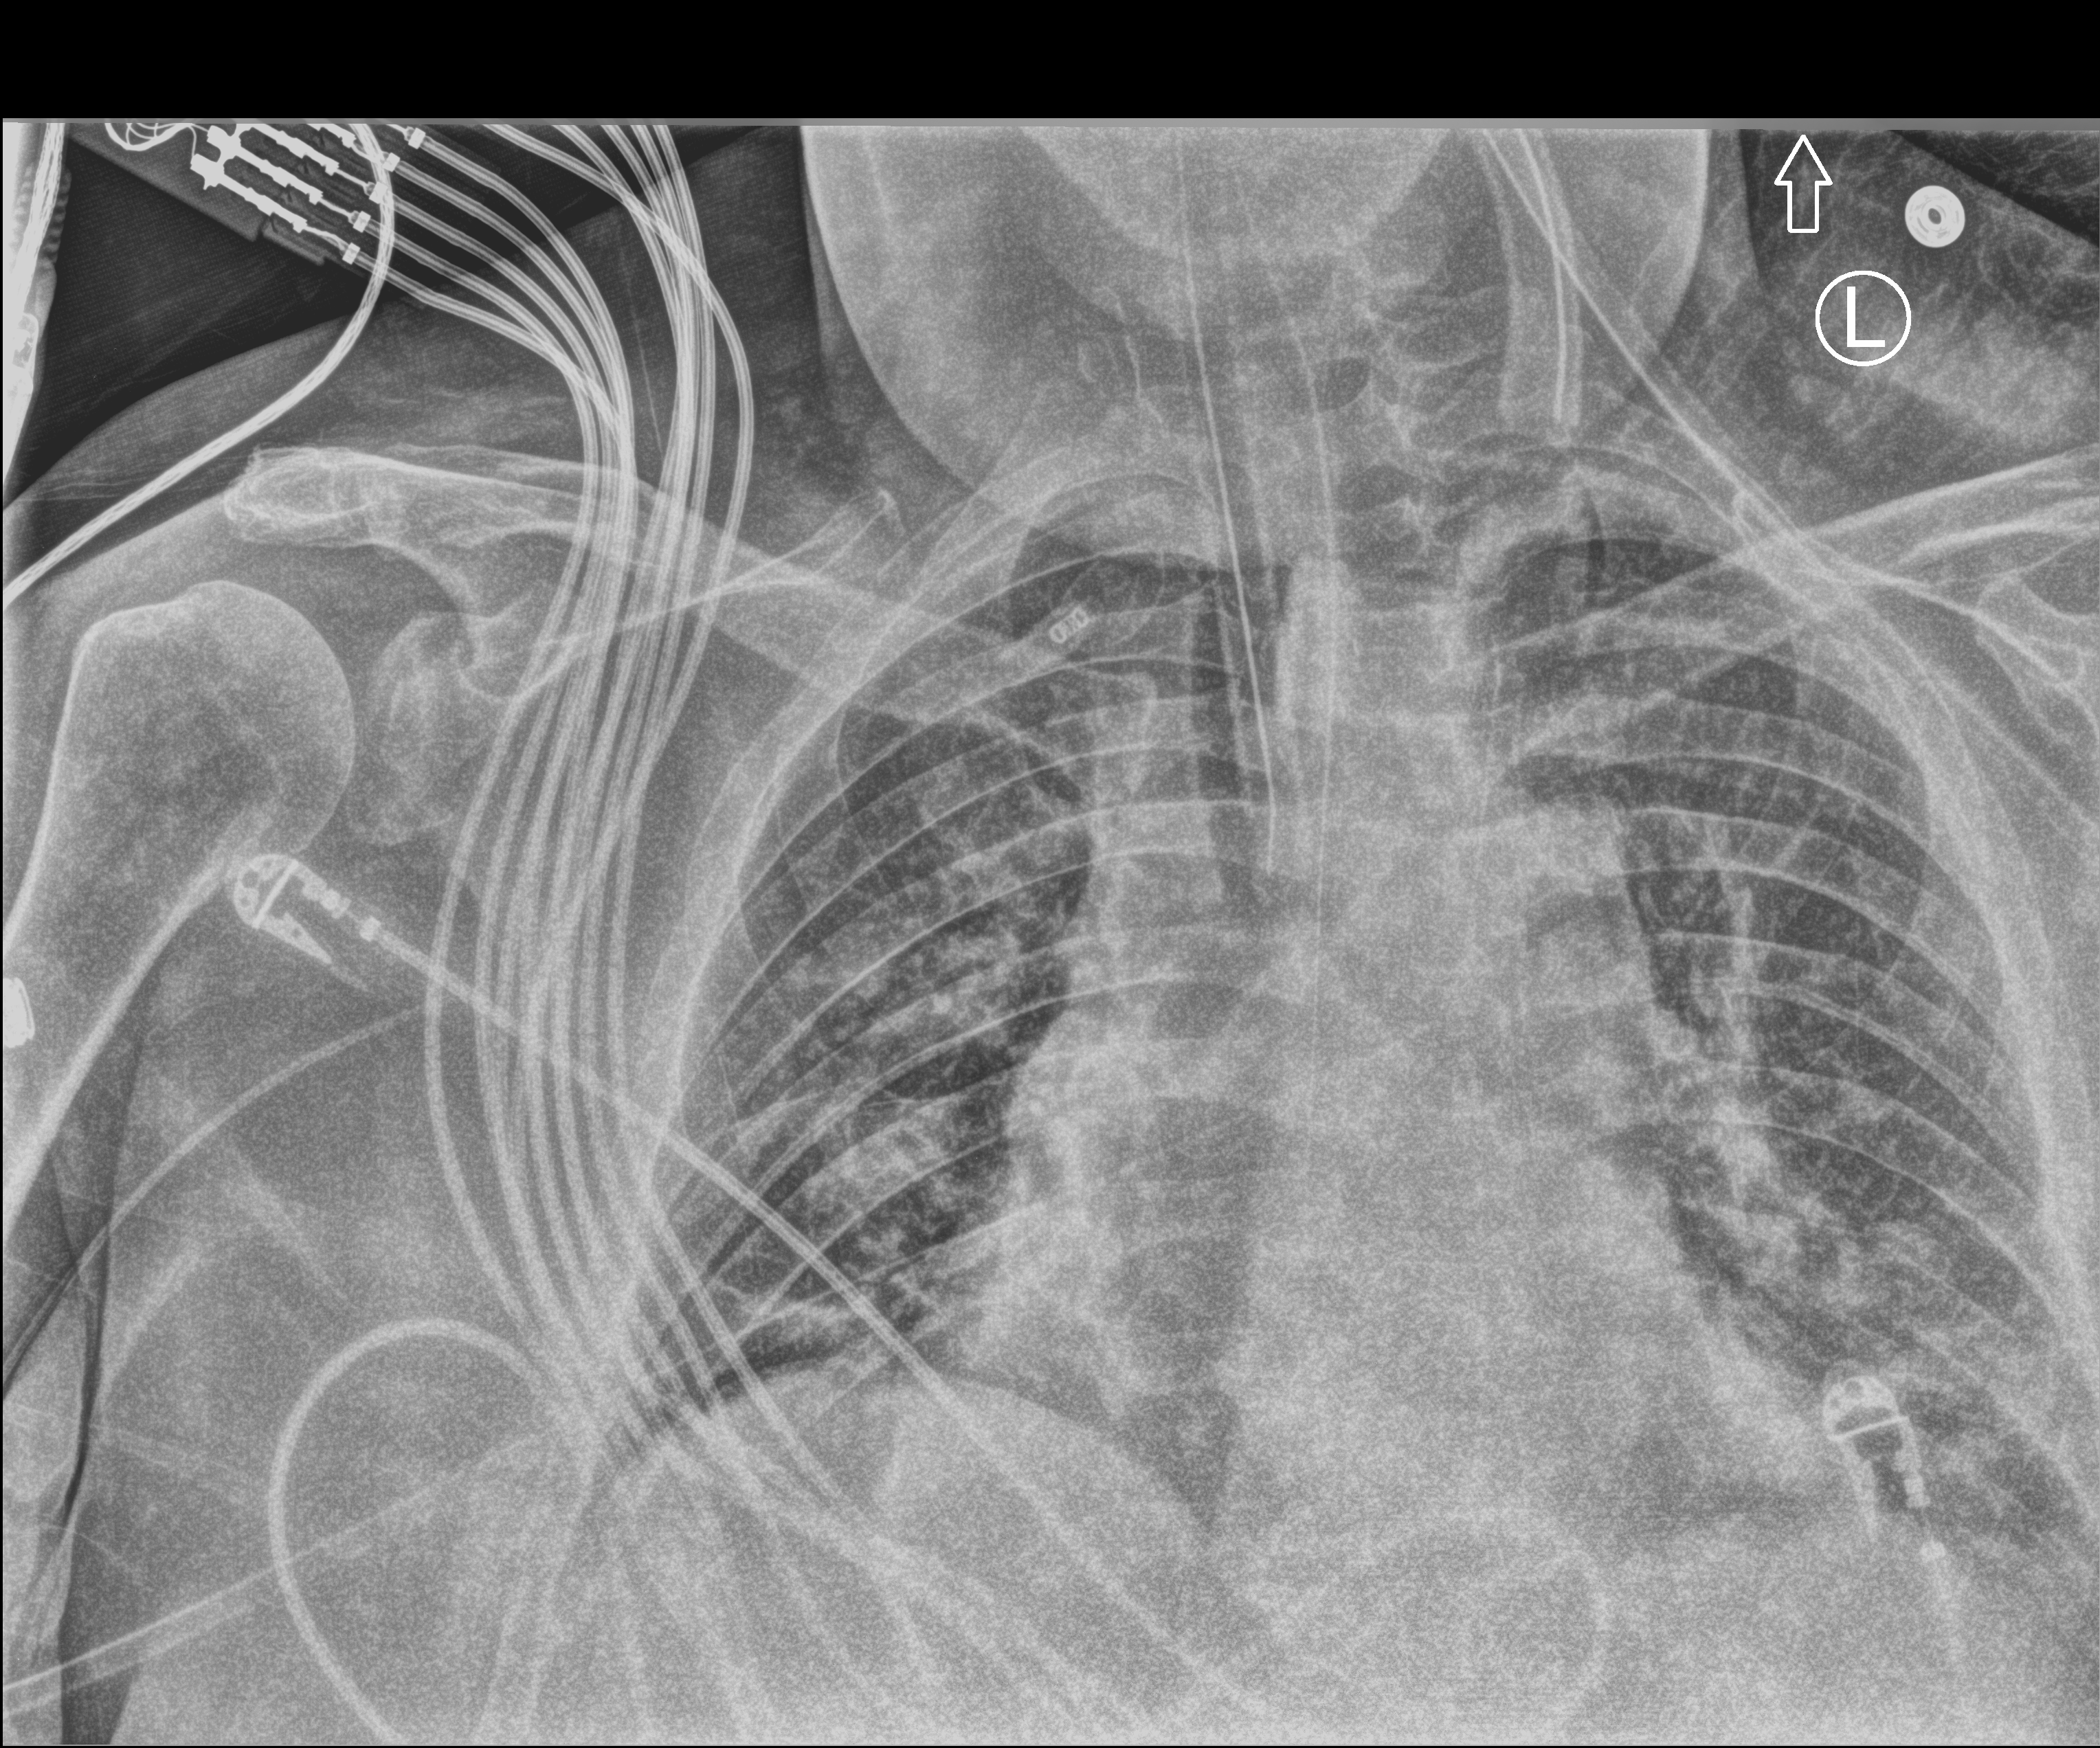
Chest X-ray (portable), anteroposterior (AP) projection. Patient hospitalised with COVID-19; male, aged 60–74 years.
Admission-level facts for this patient (not findings on this image; timing relative to this image not recorded):
- admitted to intensive care during this hospital stay: yes
- COPD (admission record): no